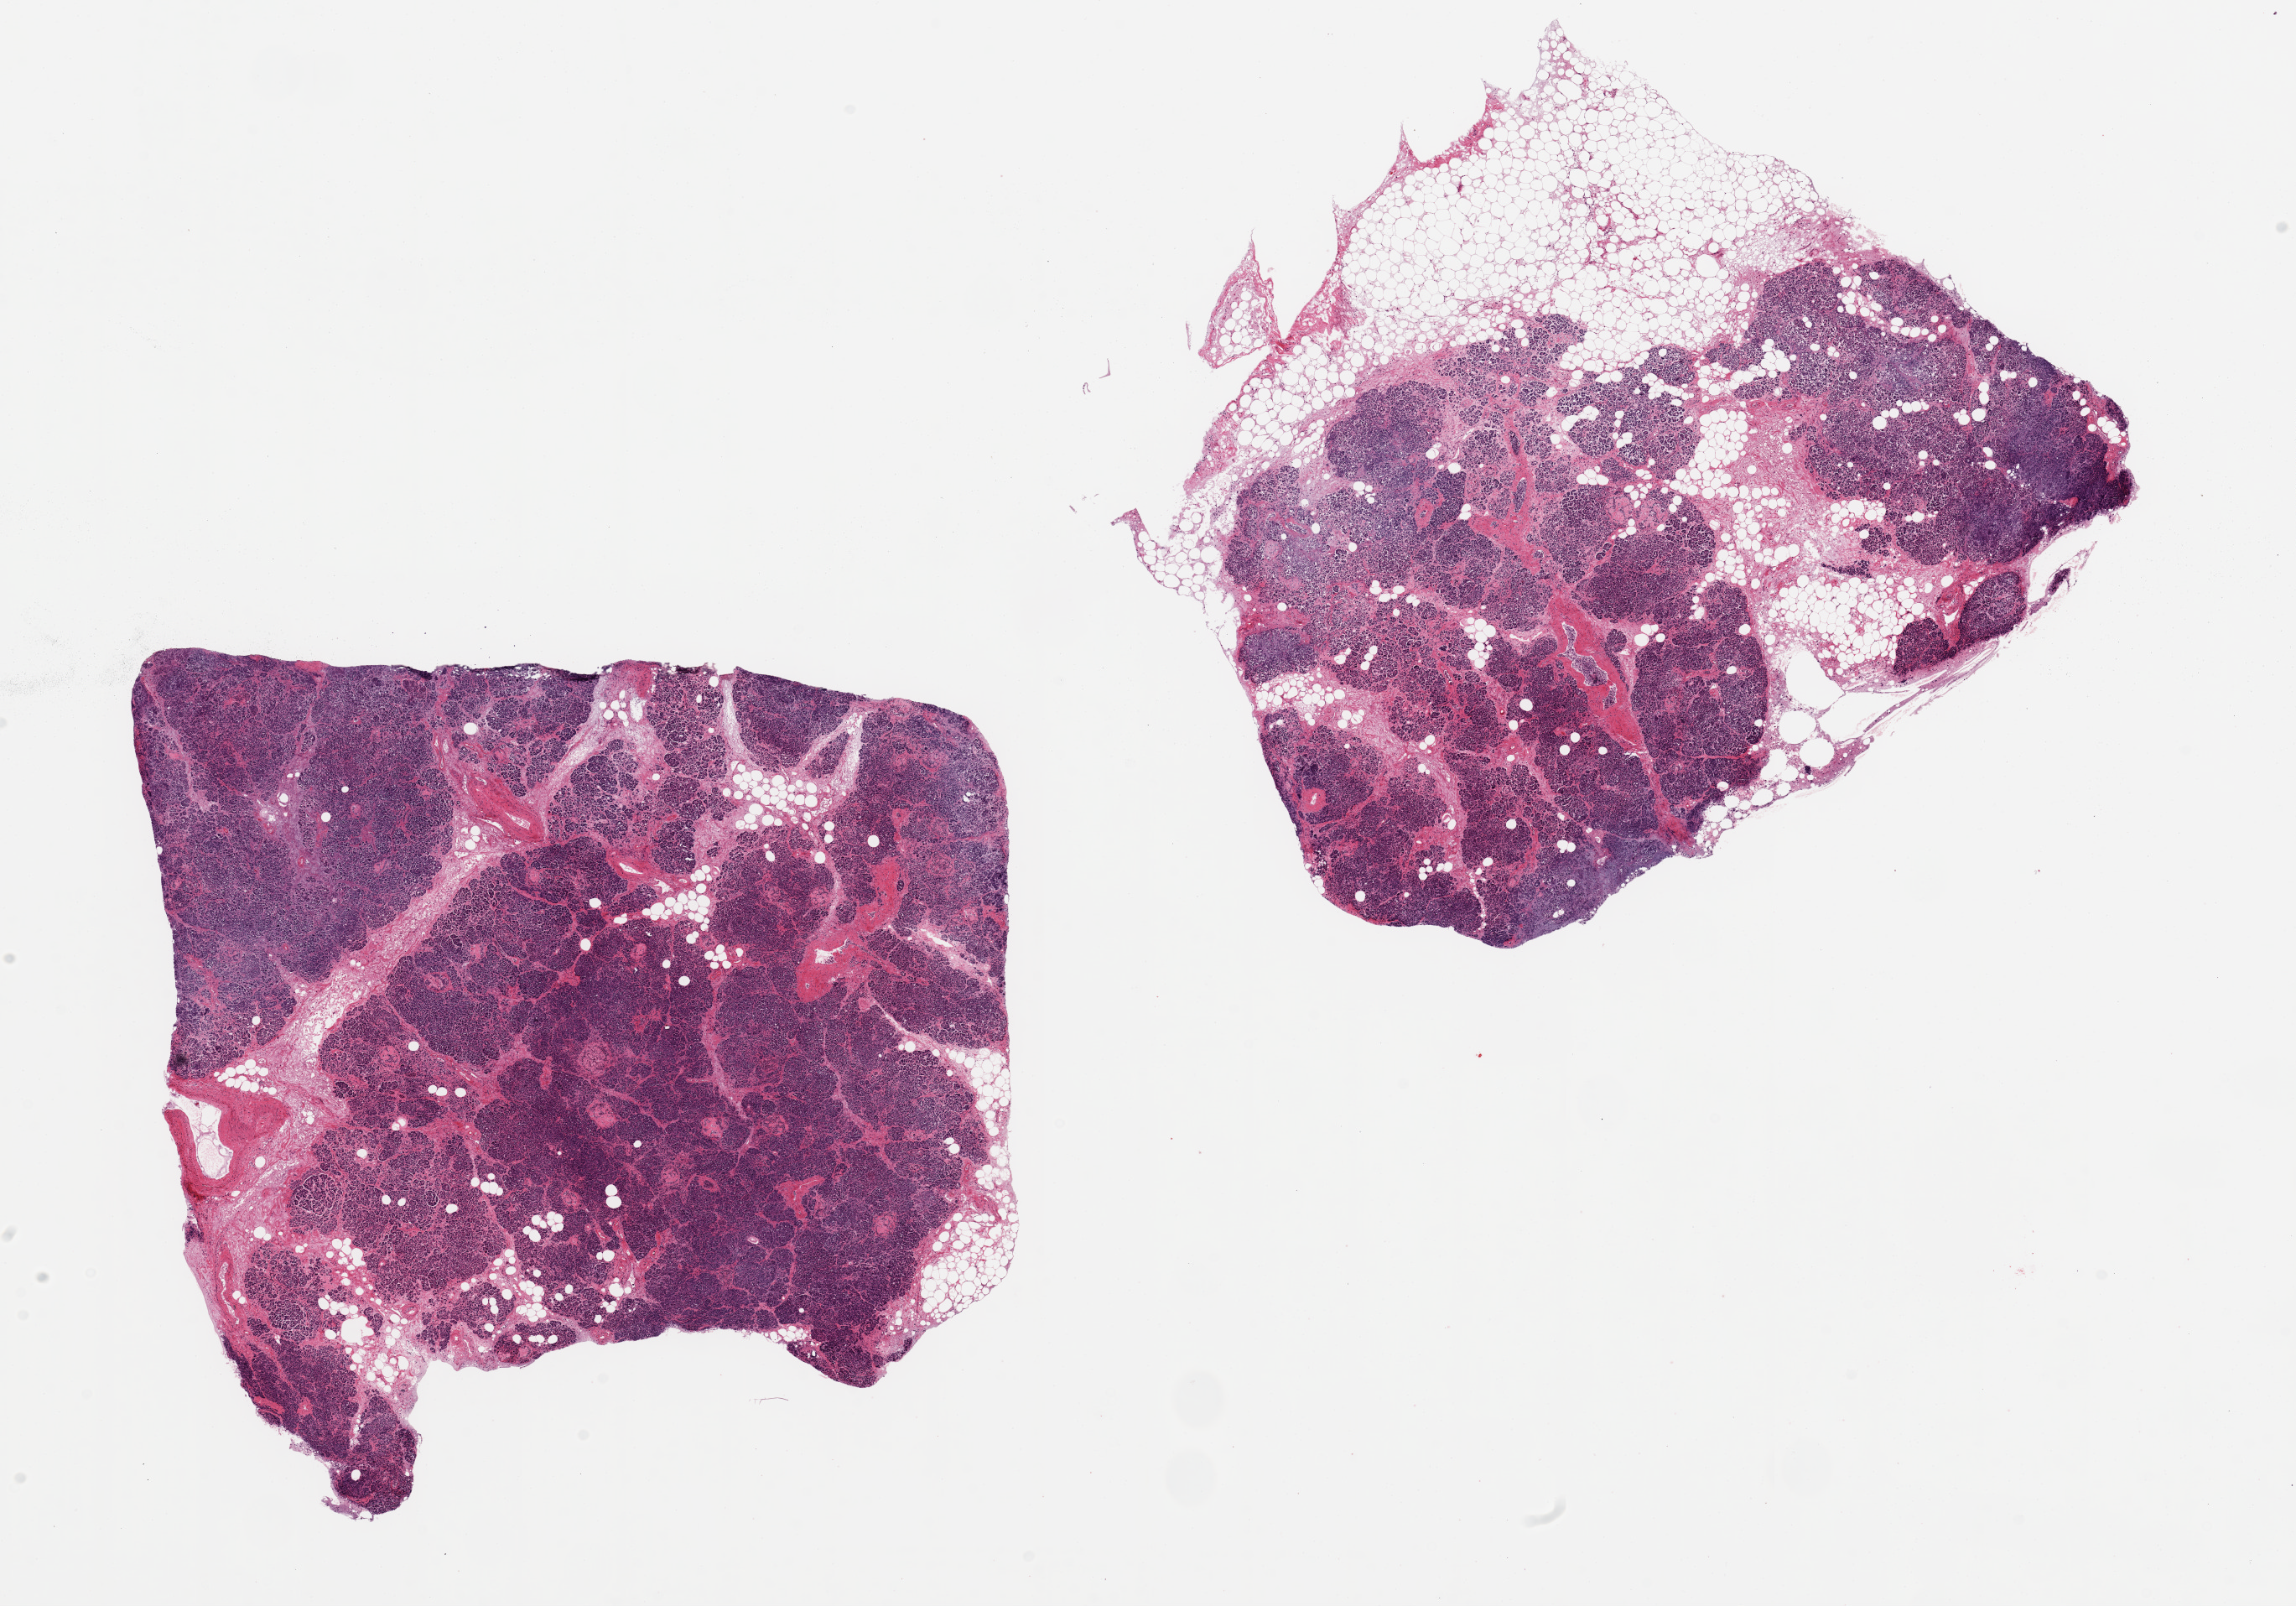
Digitized H&E-stained section, a low-resolution overview of the entire scanned area, about 21.7 x 15.1 mm. PAXgene-fixed paraffin-embedded (PFPE) section. Section of pancreas (target tissue). Donor tissue sample. Male donor.
* reviewer comment on this tissue sample: 2 aliquots, ~8x7mm. Badly autolyzed, ~30% of one aliquot is fat with saponification